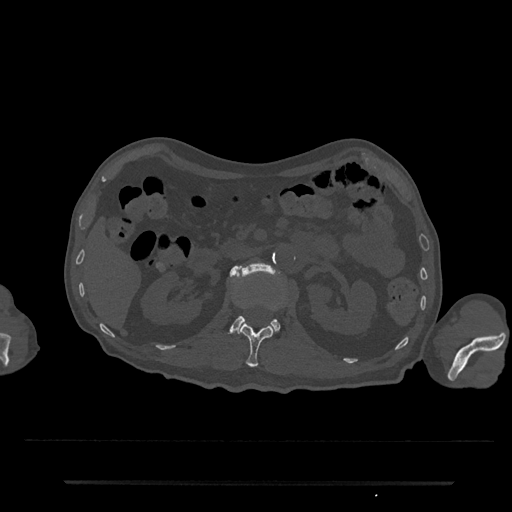
CT including the spine, one axial slice; position 103 of 797 along the scan axis; reconstruction kernel Br40s/3; 120 kVp; bone window (W 1800 / L 400 HU); 0.5 mm slice thickness; 512 × 512 image matrix. Patient: male, 74 years. Case-level facts recorded for this patient, not image findings: primary cancer: prostate.
Structures marked on this image (semi-automatically segmented with operator editing):
- L1 vertebra: bounding box <240,323,274,368> (left, top, right, bottom; pixels)
- L2 vertebra: <230,263,280,332>